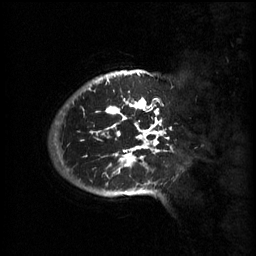
Breast MRI (dynamic contrast-enhanced), one sagittal slice. Position 50 of 60 along the scan axis. 3 images stored at this slice position (order not interpretable as contrast timing). 1.5 T. TE 4.2 ms, TR 11 ms. 2 mm slice thickness. 256 × 256 image matrix, field of view 220 × 220 mm. Female patient, age 51 years.
Structures marked on this image (semi-automatic segmentation, software-assisted and operator-edited):
- analysis volume of interest (the breast-tissue region the enhancement analysis was run in; not a lesion): bounding box (x1, y1, x2, y2) in pixels: (64, 80, 178, 199)
- tumour enhancement mask (voxels above the 70 % enhancement threshold inside the analysis volume of interest): (81, 80, 172, 193)